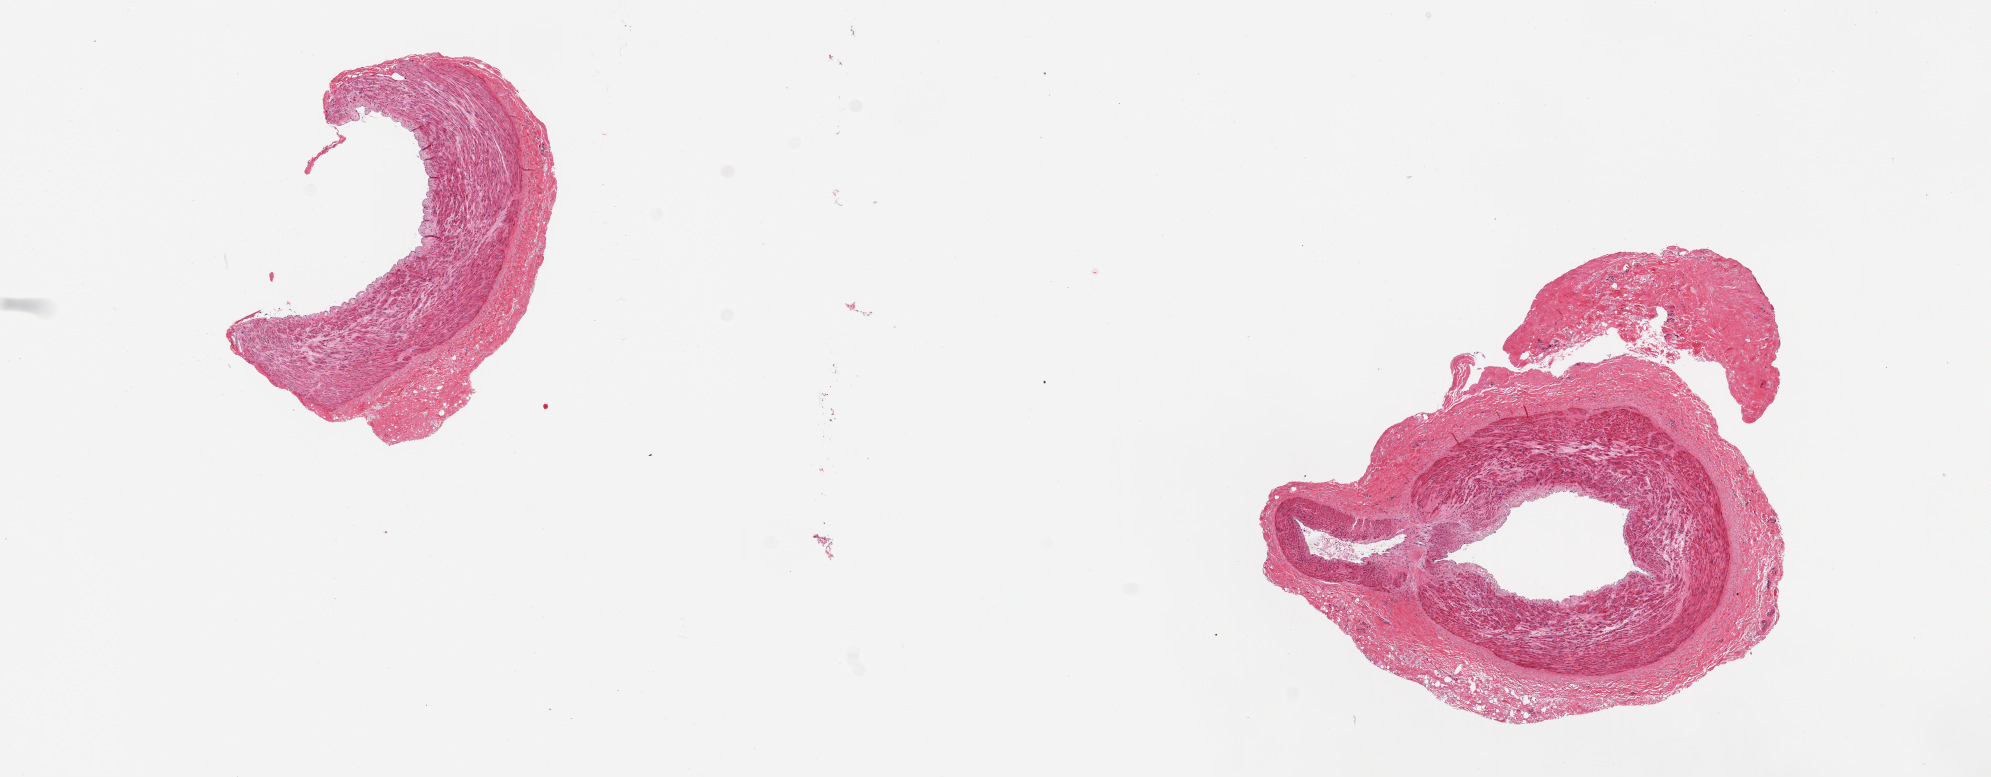
Digitized hematoxylin and eosin (H&E)-stained section, a low-resolution overview of the entire scanned area, about 15.8 x 6.1 mm (slide scanned at 20x). PAXgene-fixed paraffin-embedded (PFPE) section. Target tissue: tibial artery. Donor tissue sample. Donor: female.
• review note (as recorded): 2 pieces, 3x2 & 4x4mm; clean specimens